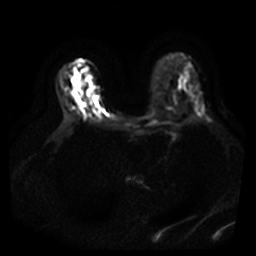
Breast MRI, one axial slice; slice 26 of 40 in the series (ordered by position); diffusion-weighted series; image 2 of 4 stored at this slice position (different b-values; order by instance number); 3 T; 5 mm slice thickness; 256 × 256 image matrix, field of view 380 × 380 mm. Female patient.
Annotated regions visible in this slice (manually delineated by an expert):
- tumour on diffusion-weighted imaging: box from (x=79, y=81) to (x=83, y=89) px